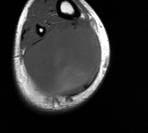
MRI of an extremity soft-tissue mass, one axial slice; position 42 of 76 along the scan axis; MR volume resampled by the dataset authors to the PET/CT grid (not the native acquisition matrix); 148 × 133 image matrix, field of view 145 × 130 mm. Male patient. From the clinical record (not read from this slice): histological type: liposarcoma - round cell; grade: high; site of the primary tumour: right calf.
Structures marked on this image (expert contour drawn on MRI and transferred to this co-registered scan by the dataset authors):
- gross tumour volume (mass): box from (x=26, y=26) to (x=101, y=95) px